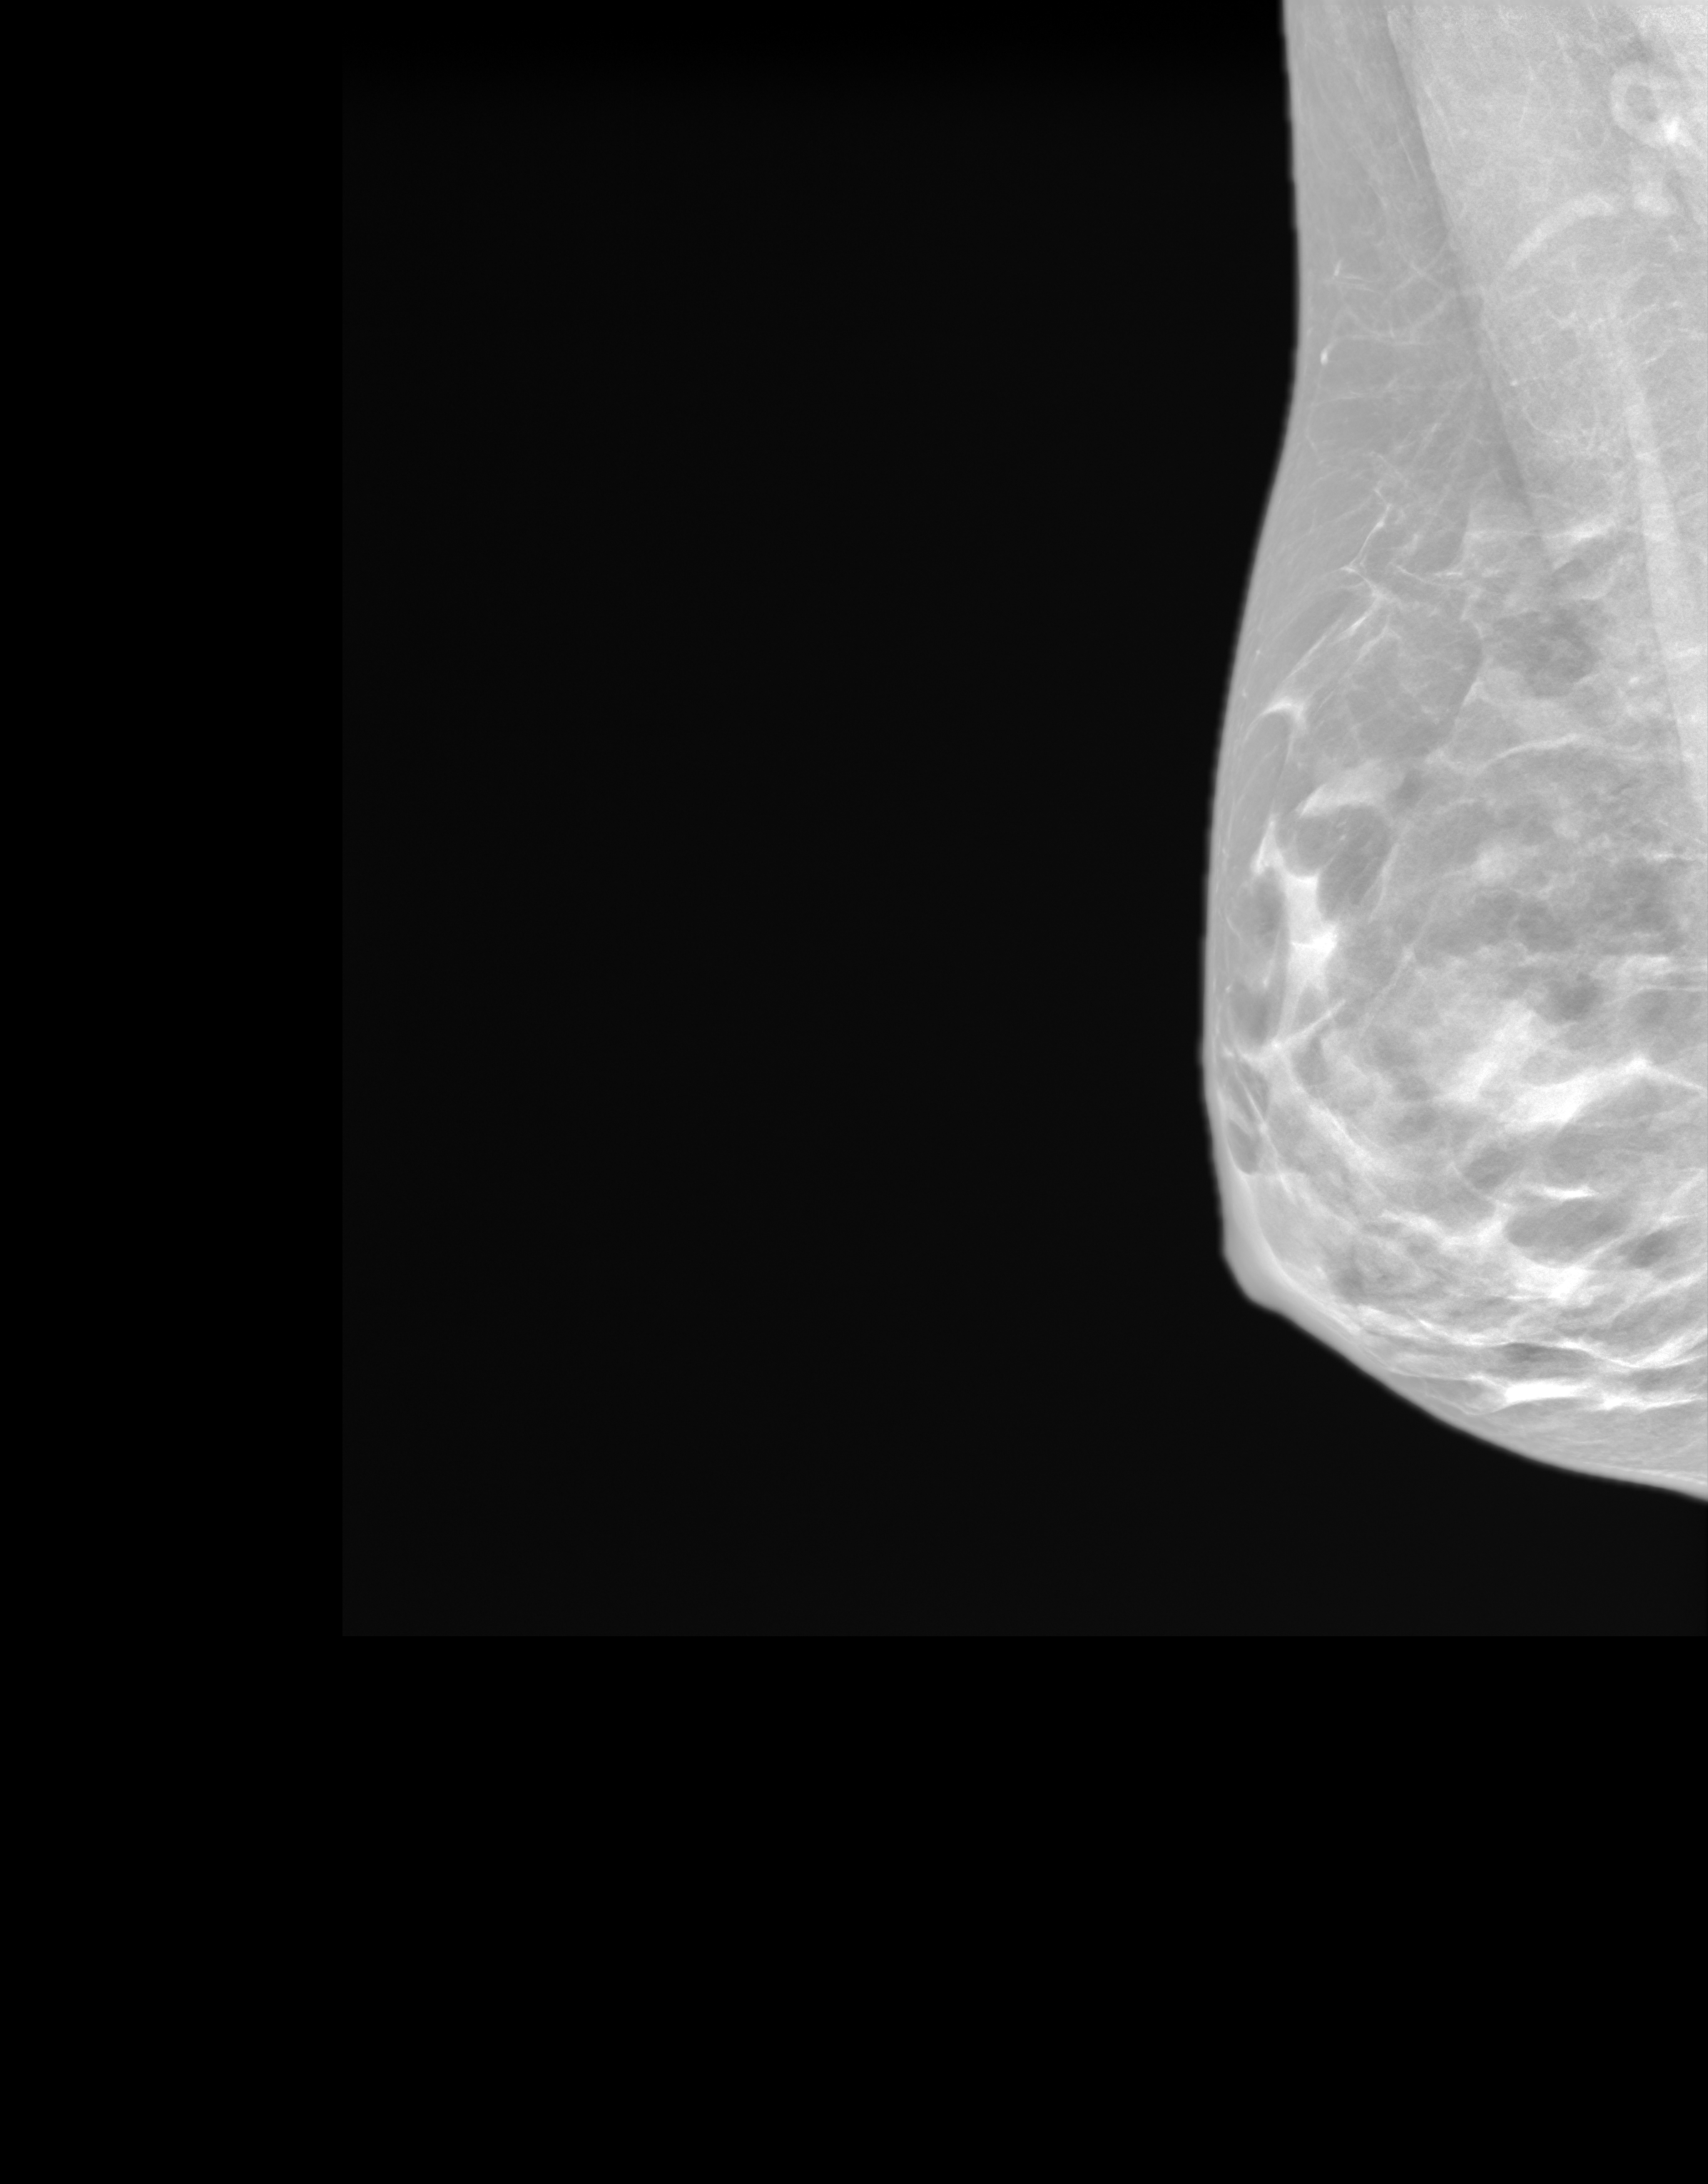
Synthetic 2-D view generated from a tomosynthesis acquisition (not an FFDM exposure), right breast, mediolateral oblique (MLO) view, screening examination, system: SenoIris_1SP1.1(421). Patient: female, 66 years.
- BI-RADS breast density category at the screening exam (both breasts, scale 1–4): 3
- final BI-RADS assessment for this screening round (tomosynthesis exam, both breasts): category 1
- recall: no recall after this screen